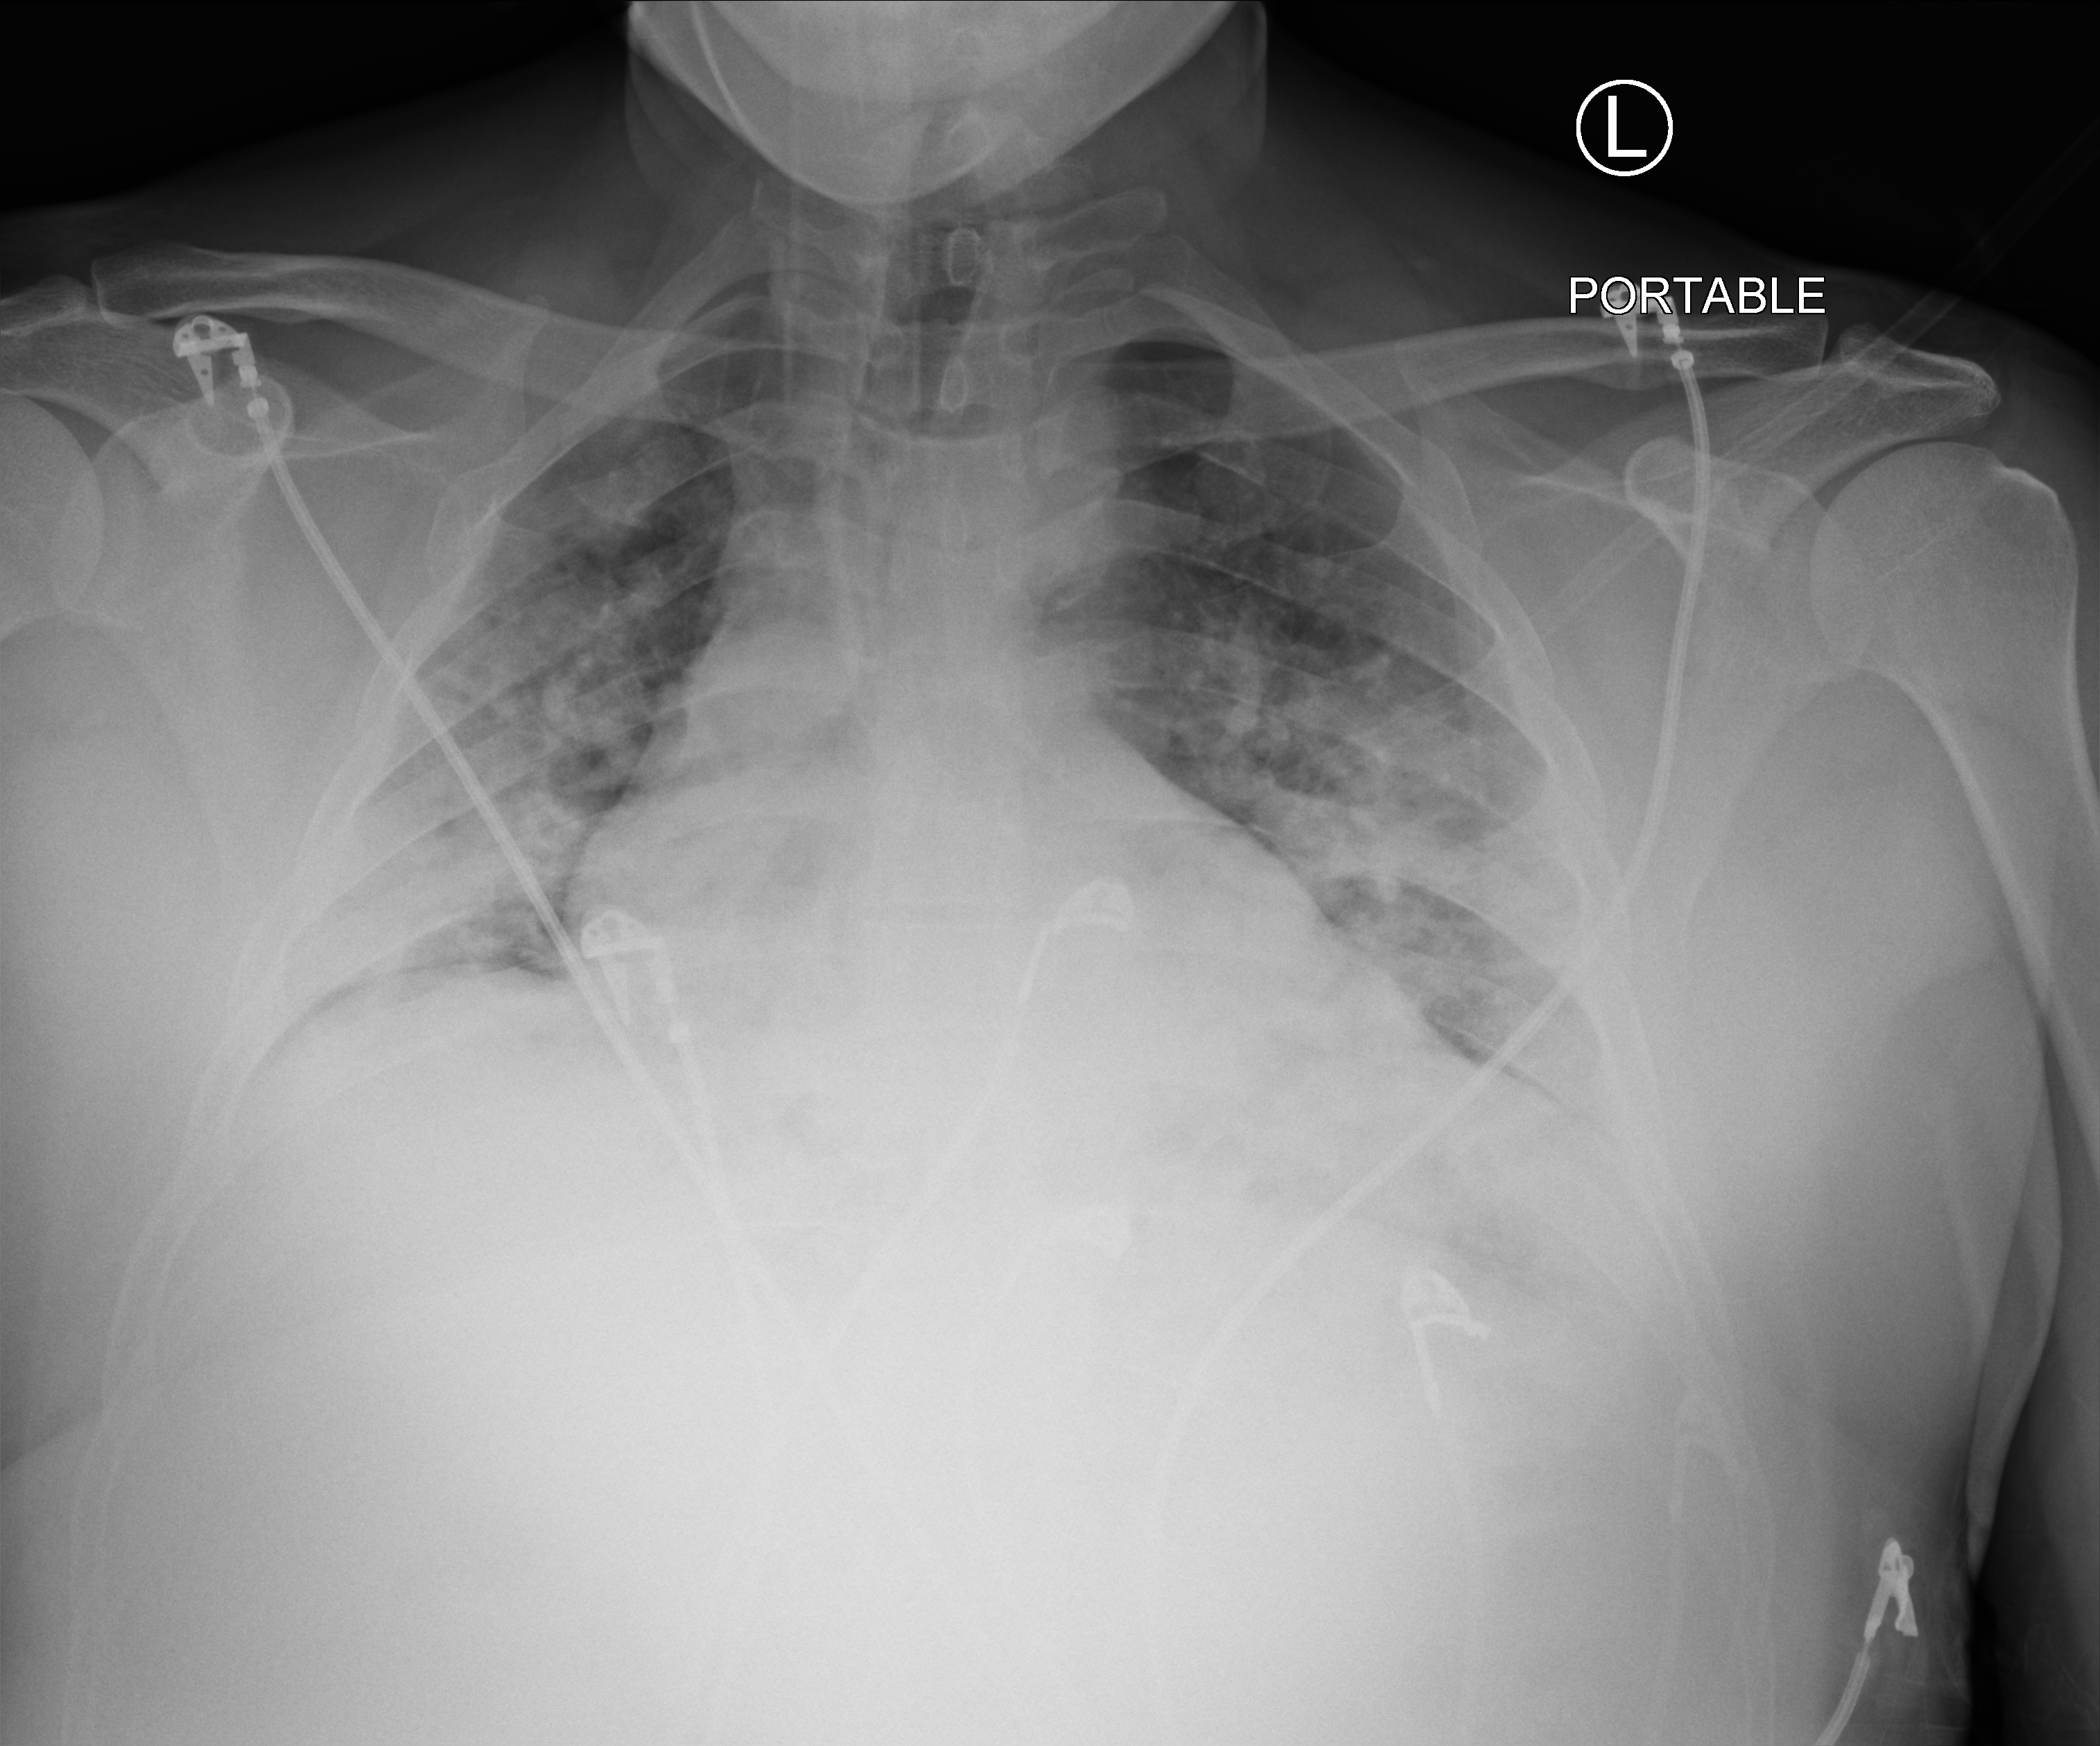
Chest X-ray (portable), anteroposterior (AP) projection. Patient hospitalised with COVID-19; male, aged 18–59 years.
Hospital-stay facts (about this admission, not read from this image; timing relative to this image not recorded):
- COPD (admission record): no
- length of hospital stay: 11 days
- admitted to intensive care during this hospital stay: no